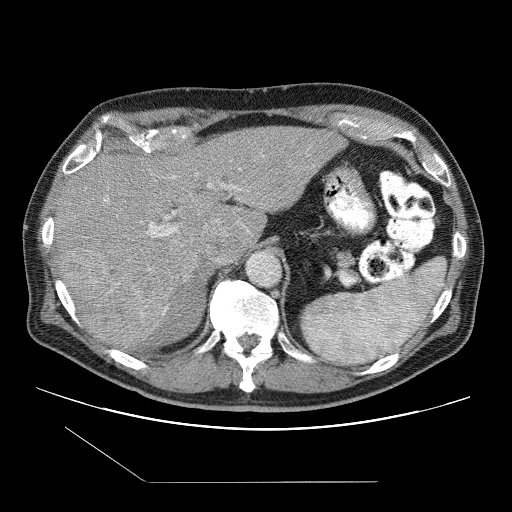
Contrast-enhanced abdominal CT (liver protocol), one axial slice; slice 70 of 109 in the series (ordered by position); 120 kVp; one of 2 acquisitions stored at this slice position; soft-tissue window (W 400 / L 40 HU); 2.5 mm slice thickness; 512 × 512 image matrix, field of view 400 × 400 mm. Case-level facts recorded for this patient, not image findings: diagnosis: hepatocellular carcinoma (patient treated with transarterial chemoembolisation; whether this scan precedes or follows treatment is not stated here); TNM stage (as recorded): Stage-IIIB; Child-Pugh class: A; tumour nodularity: multinodular.
Annotated regions visible in this slice (semi-automatic segmentation, software-assisted and operator-edited):
- abdominal aorta: bounding box [x1, y1, x2, y2] px = [246, 251, 280, 286]
- liver parenchyma outside the tumour (the mass and vessels are separate outlines, so this box may not span the whole liver): [54, 126, 344, 348]
- mass: [61, 243, 194, 350]
- liver vessels: [107, 176, 249, 237]